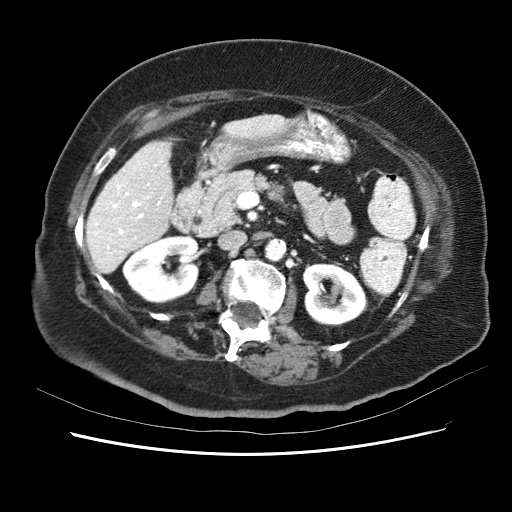
Contrast-enhanced abdominal CT (liver protocol), one axial slice; slice 20 of 62 in the series (ordered by position); reconstruction kernel STANDARD; soft-tissue window (W 400 / L 40 HU); 2.5 mm slice thickness; 512 × 512 image matrix, field of view 340 × 340 mm. Case-level facts recorded for this patient, not image findings: diagnosis: hepatocellular carcinoma (patient treated with transarterial chemoembolisation; whether this scan precedes or follows treatment is not stated here); TNM stage (as recorded): Stage-I; Child-Pugh class: B.
Outlined on this slice (semi-automatic segmentation, software-assisted and operator-edited):
- liver parenchyma outside the tumour (the mass and vessels are separate outlines, so this box may not span the whole liver): bounding box (x1, y1, x2, y2) in pixels: (86, 112, 330, 274)
- liver vessels: (89, 121, 289, 268)